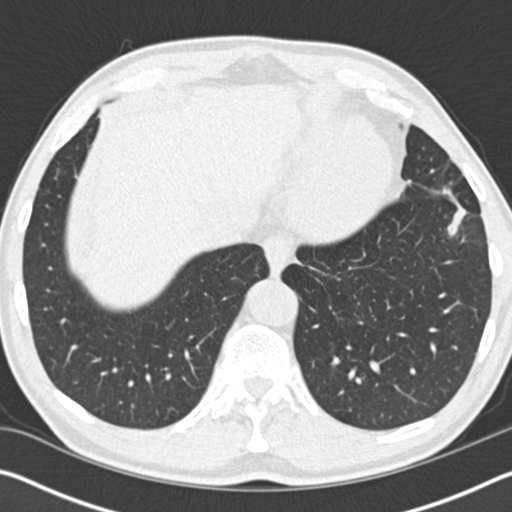
Low-dose screening chest CT, one axial slice; position 36 of 162 along the scan axis; reconstruction kernel B30f; lung window (W 1500 / L -600 HU); 512 × 512 image matrix, field of view 340 × 340 mm.
Outlined on this slice (manually delineated by an expert):
- lesion 1 (tumor, upper lobe of left lung): bounding box <440,187,468,237> (left, top, right, bottom; pixels)